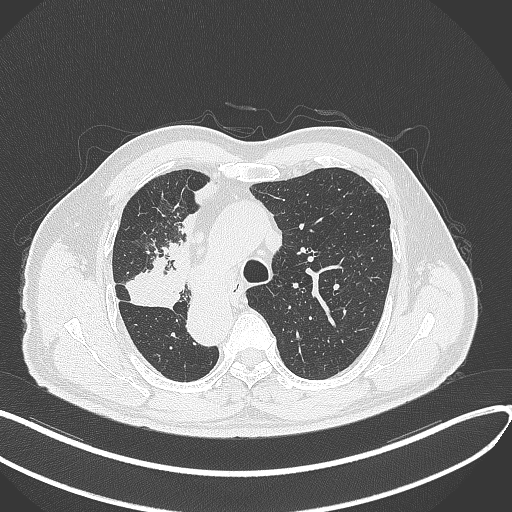
Chest CT, one axial slice. Position 223 of 300 along the scan axis. Reconstruction kernel B70f. Lung window (W 1500 / L -600 HU). 512 × 512 image matrix. Male patient, age 67 years. Case-level facts recorded for this patient, not image findings: clinical TNM (as recorded): T2a N0 M0.
Outlined on this slice (rectangle marked by the reading radiologist):
- lung tumour (recorded histology: squamous cell carcinoma): box from (x=125, y=252) to (x=188, y=312) px